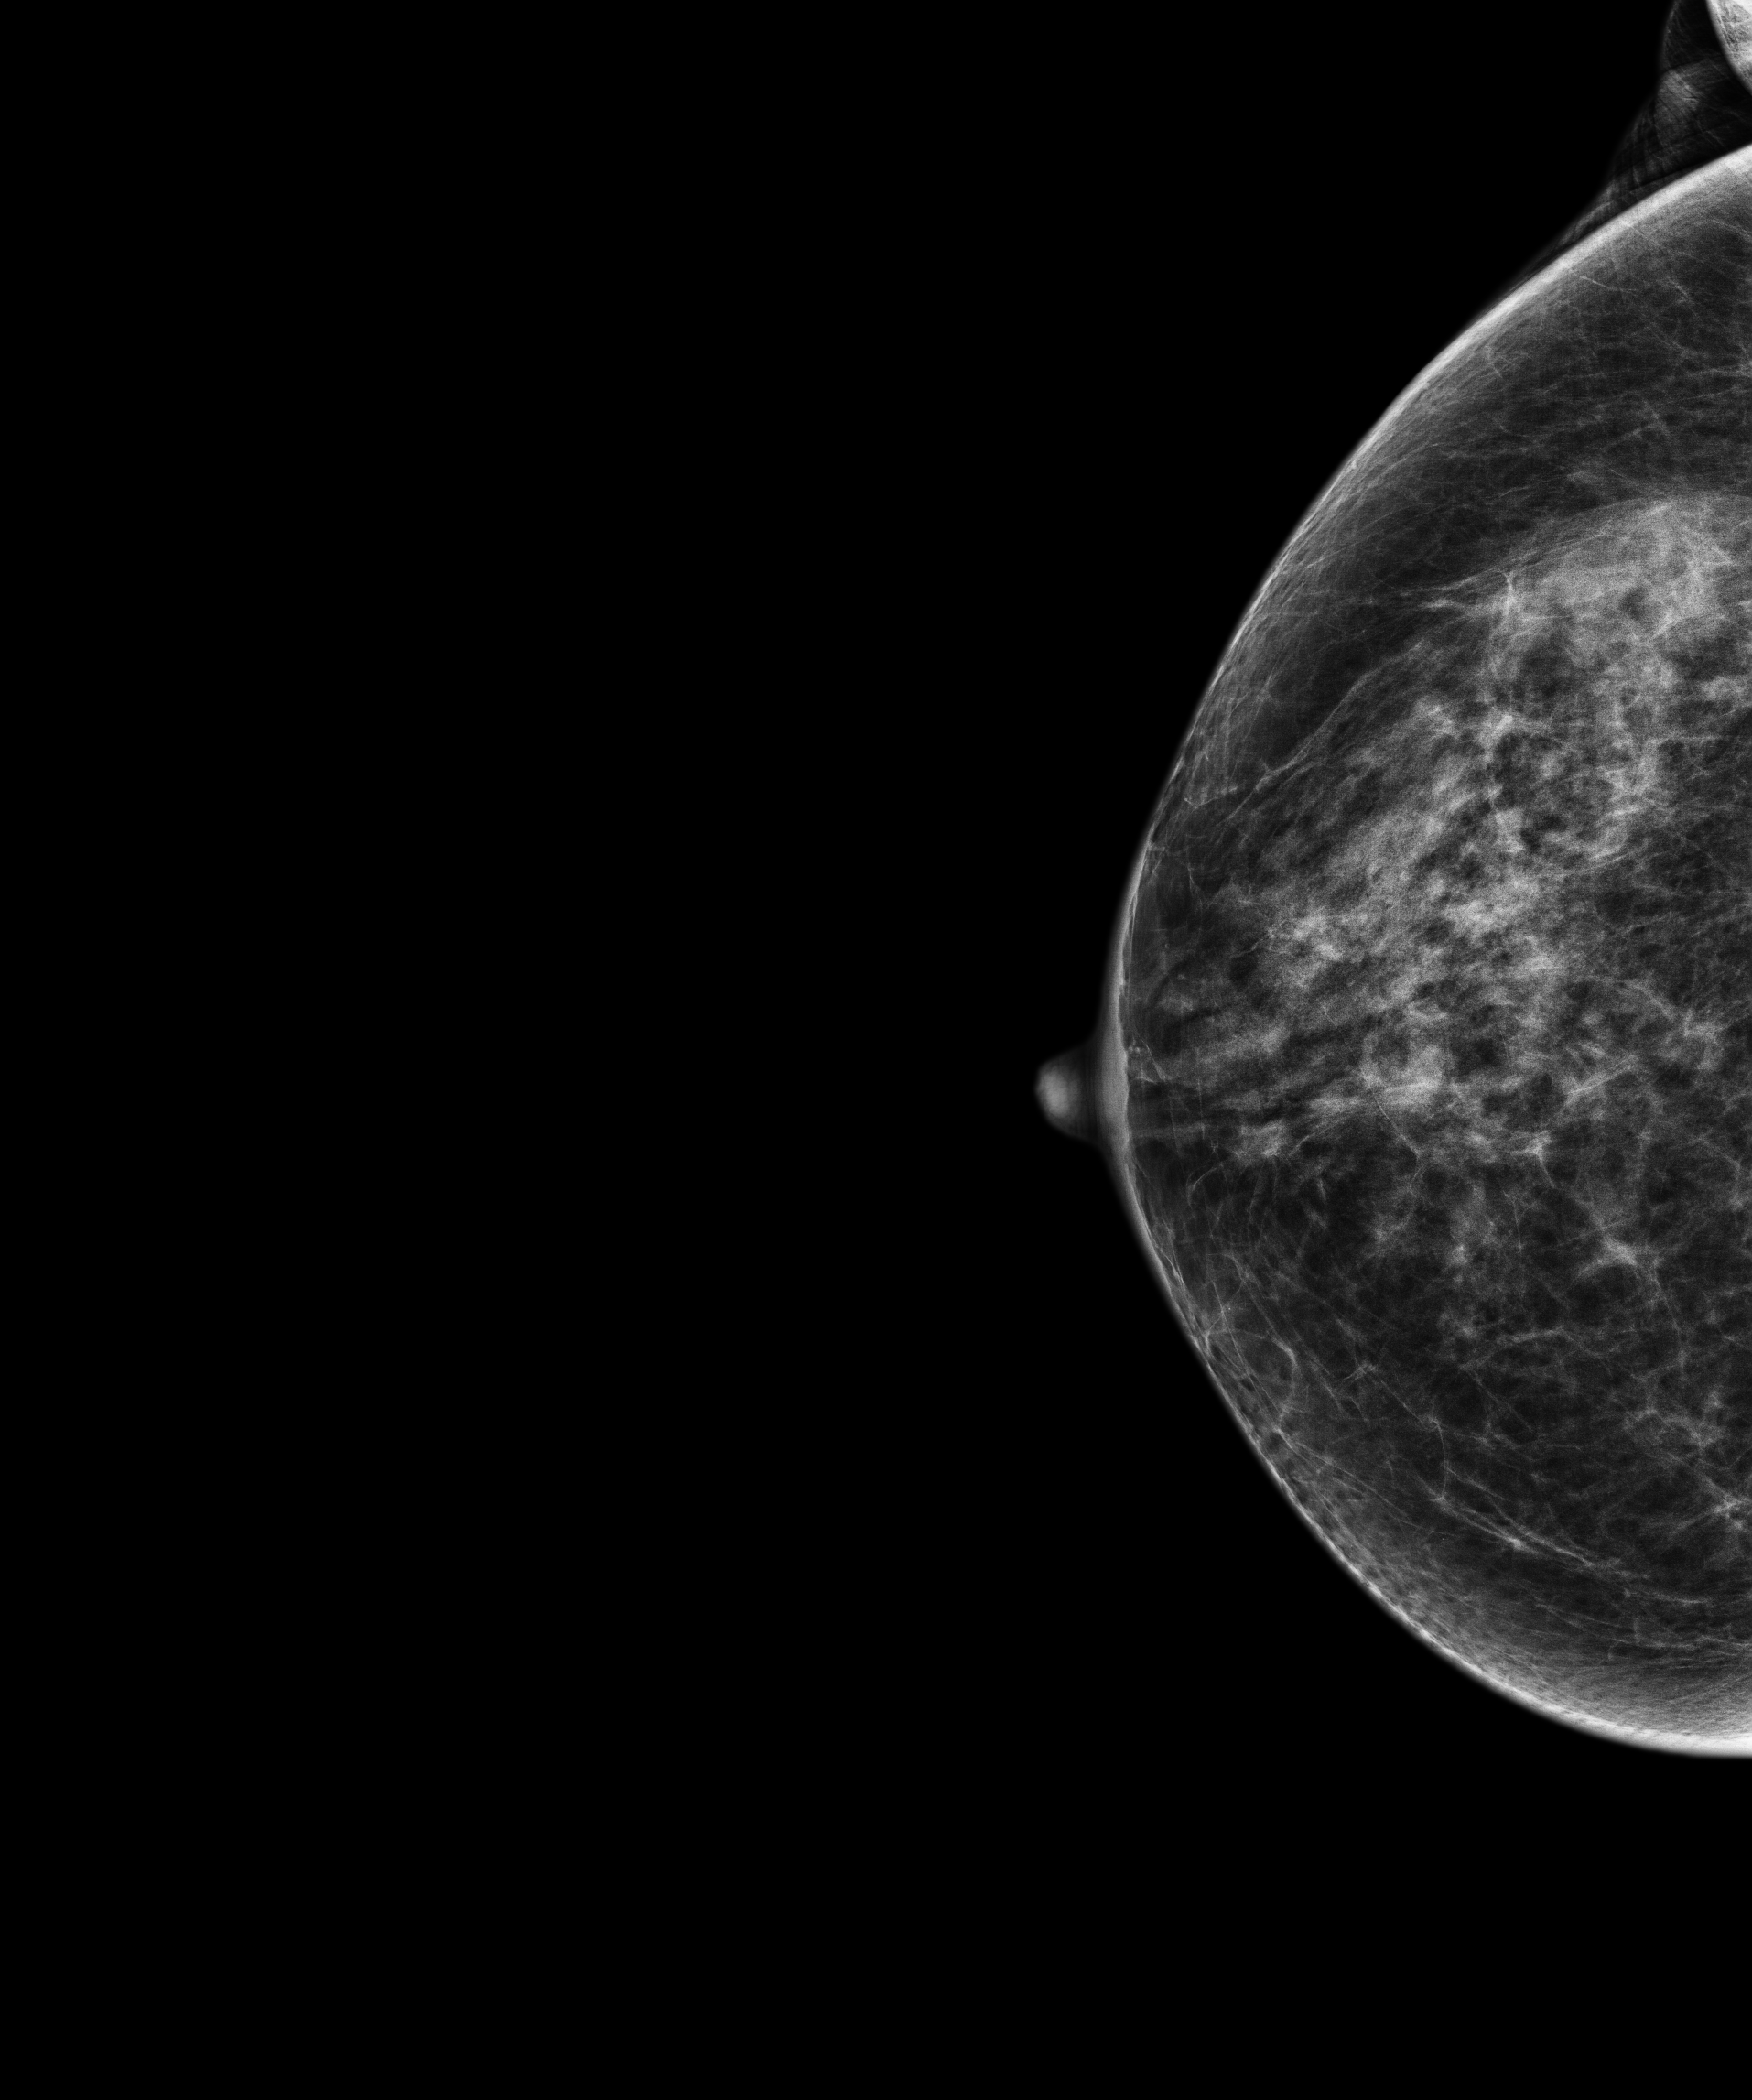
Annual screening mammography examination, compressed breast thickness 60.2 mm, system: Senographe Pristina. Patient: female, 62 years.
Image type: full-field digital mammogram. Breast: right. Projection: cranio-caudal projection.